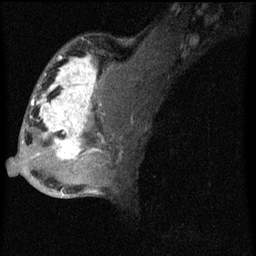
Breast MRI (dynamic contrast-enhanced), one sagittal slice. Position 35 of 60 along the scan axis. Dynamic contrast-enhanced series, image 2 of 4 at this slice position (ordered by acquisition). 1.5 T. TE 4.2 ms, TR 8 ms. 2 mm slice thickness. 256 × 256 image matrix. Patient: female, 50 years.
Annotated regions visible in this slice (semi-automatically segmented with operator editing):
- analysis volume of interest (the breast-tissue region the enhancement analysis was run in; not a lesion): bounding box (x1, y1, x2, y2) in pixels: (26, 44, 124, 177)
- tumour enhancement mask (voxels above the 70 % enhancement threshold inside the analysis volume of interest): (31, 54, 103, 161)